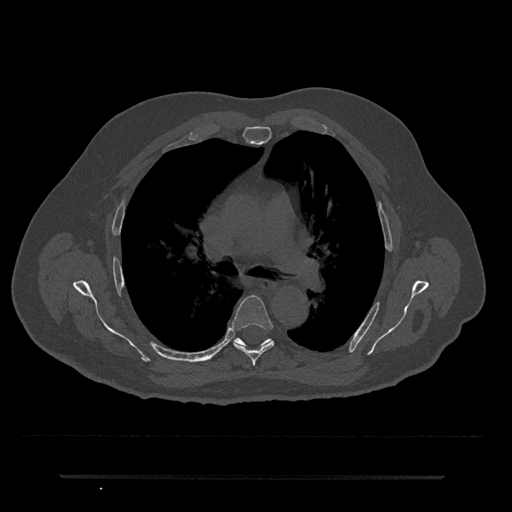
CT including the spine, one axial slice; slice 470 of 797 in the series (ordered by position); reconstruction kernel Br40s/3; bone window (W 1800 / L 400 HU); 0.5 mm slice thickness; 512 × 512 image matrix, field of view 437 × 437 mm. Patient: male, 69 years. From the clinical record (not read from this slice): primary cancer: prostate.
Outlined on this slice (semi-automatic segmentation, software-assisted and operator-edited):
- T5 vertebra: bounding box (x1, y1, x2, y2) in pixels: (231, 295, 274, 366)
- T6 vertebra: (235, 338, 243, 345)